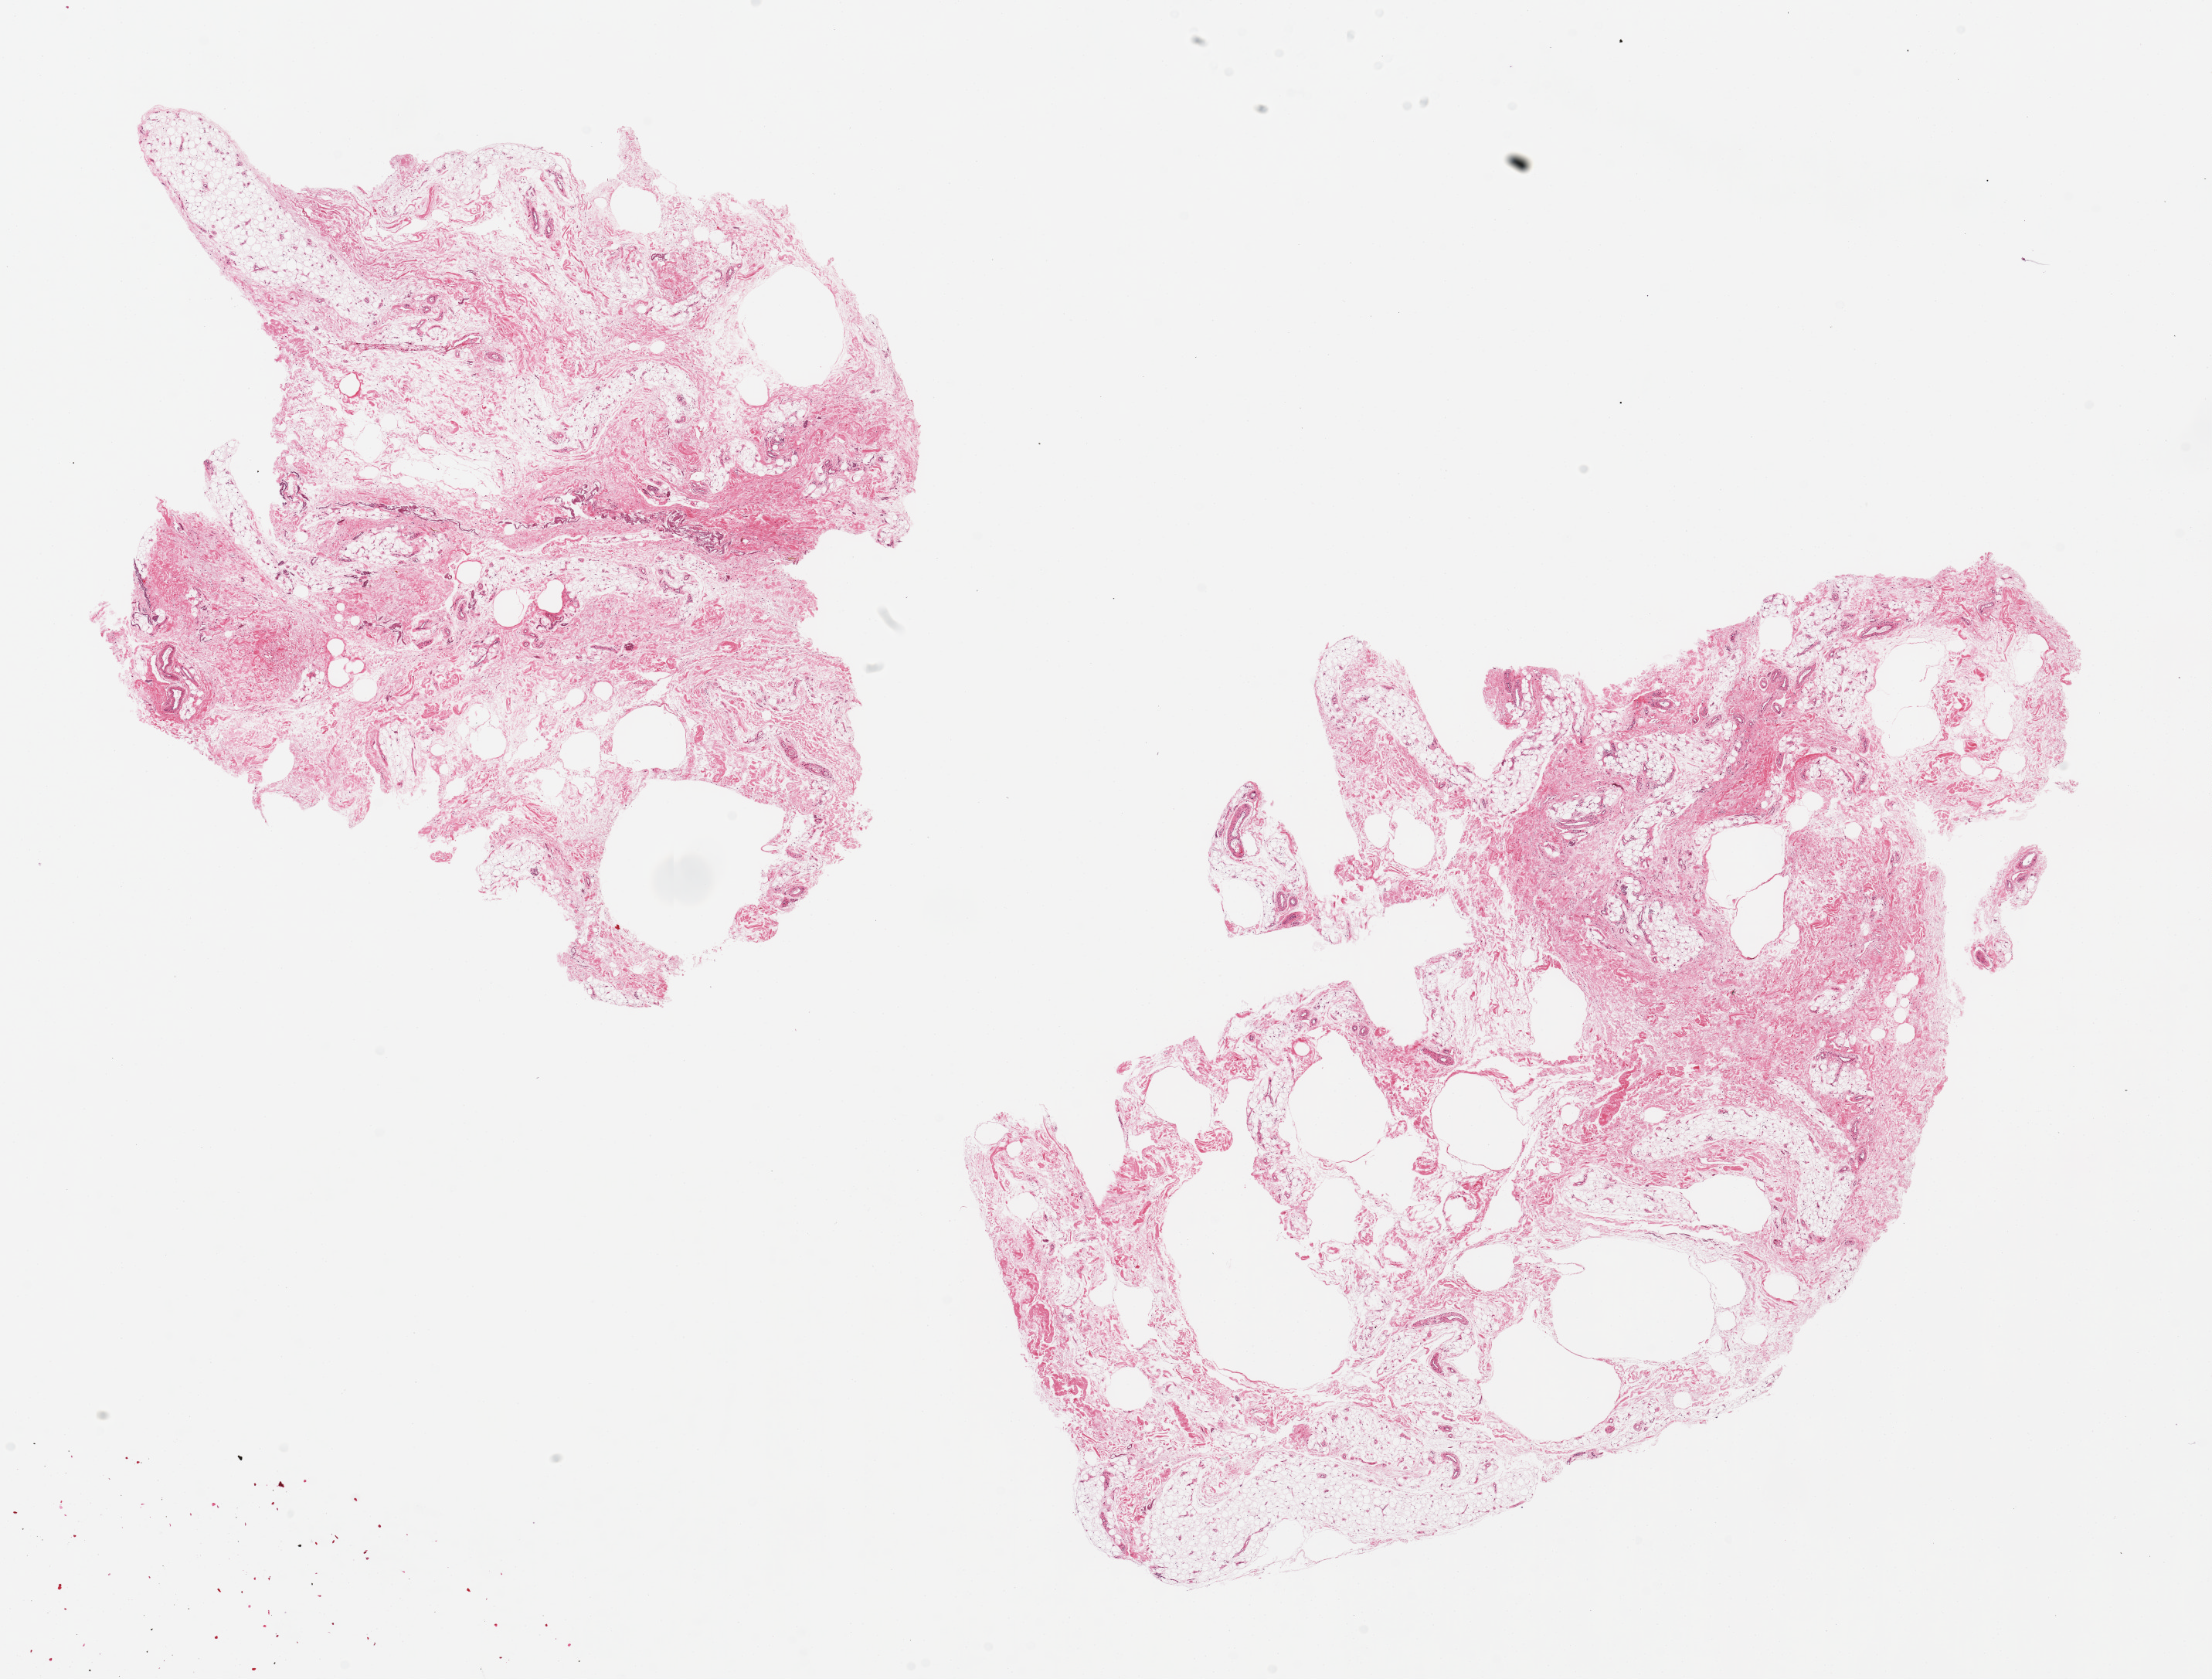
H&E whole-slide image — low-resolution overview of the scanned area, about 22.6 x 17.2 mm (from a 20x scan), PAXgene-fixed paraffin-embedded (PFPE) section, target tissue: adipose tissue, tissue donor sample. Donor: male.
- review note (as recorded): 2 pieces 13x6 & 7x7 mm; fibroadipose tissue with large fatty vacuoles